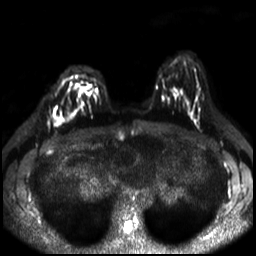
Breast MRI, one axial slice; slice 15 of 30 in the series (ordered by position); diffusion-weighted series; image 2 of 4 stored at this slice position (different b-values; order by instance number); 3 T; 256 × 256 image matrix, field of view 320 × 320 mm. Female patient.
Outlined on this slice (manually delineated by an expert):
- tumour on diffusion-weighted imaging: bounding box [x1, y1, x2, y2] px = [55, 116, 63, 121]